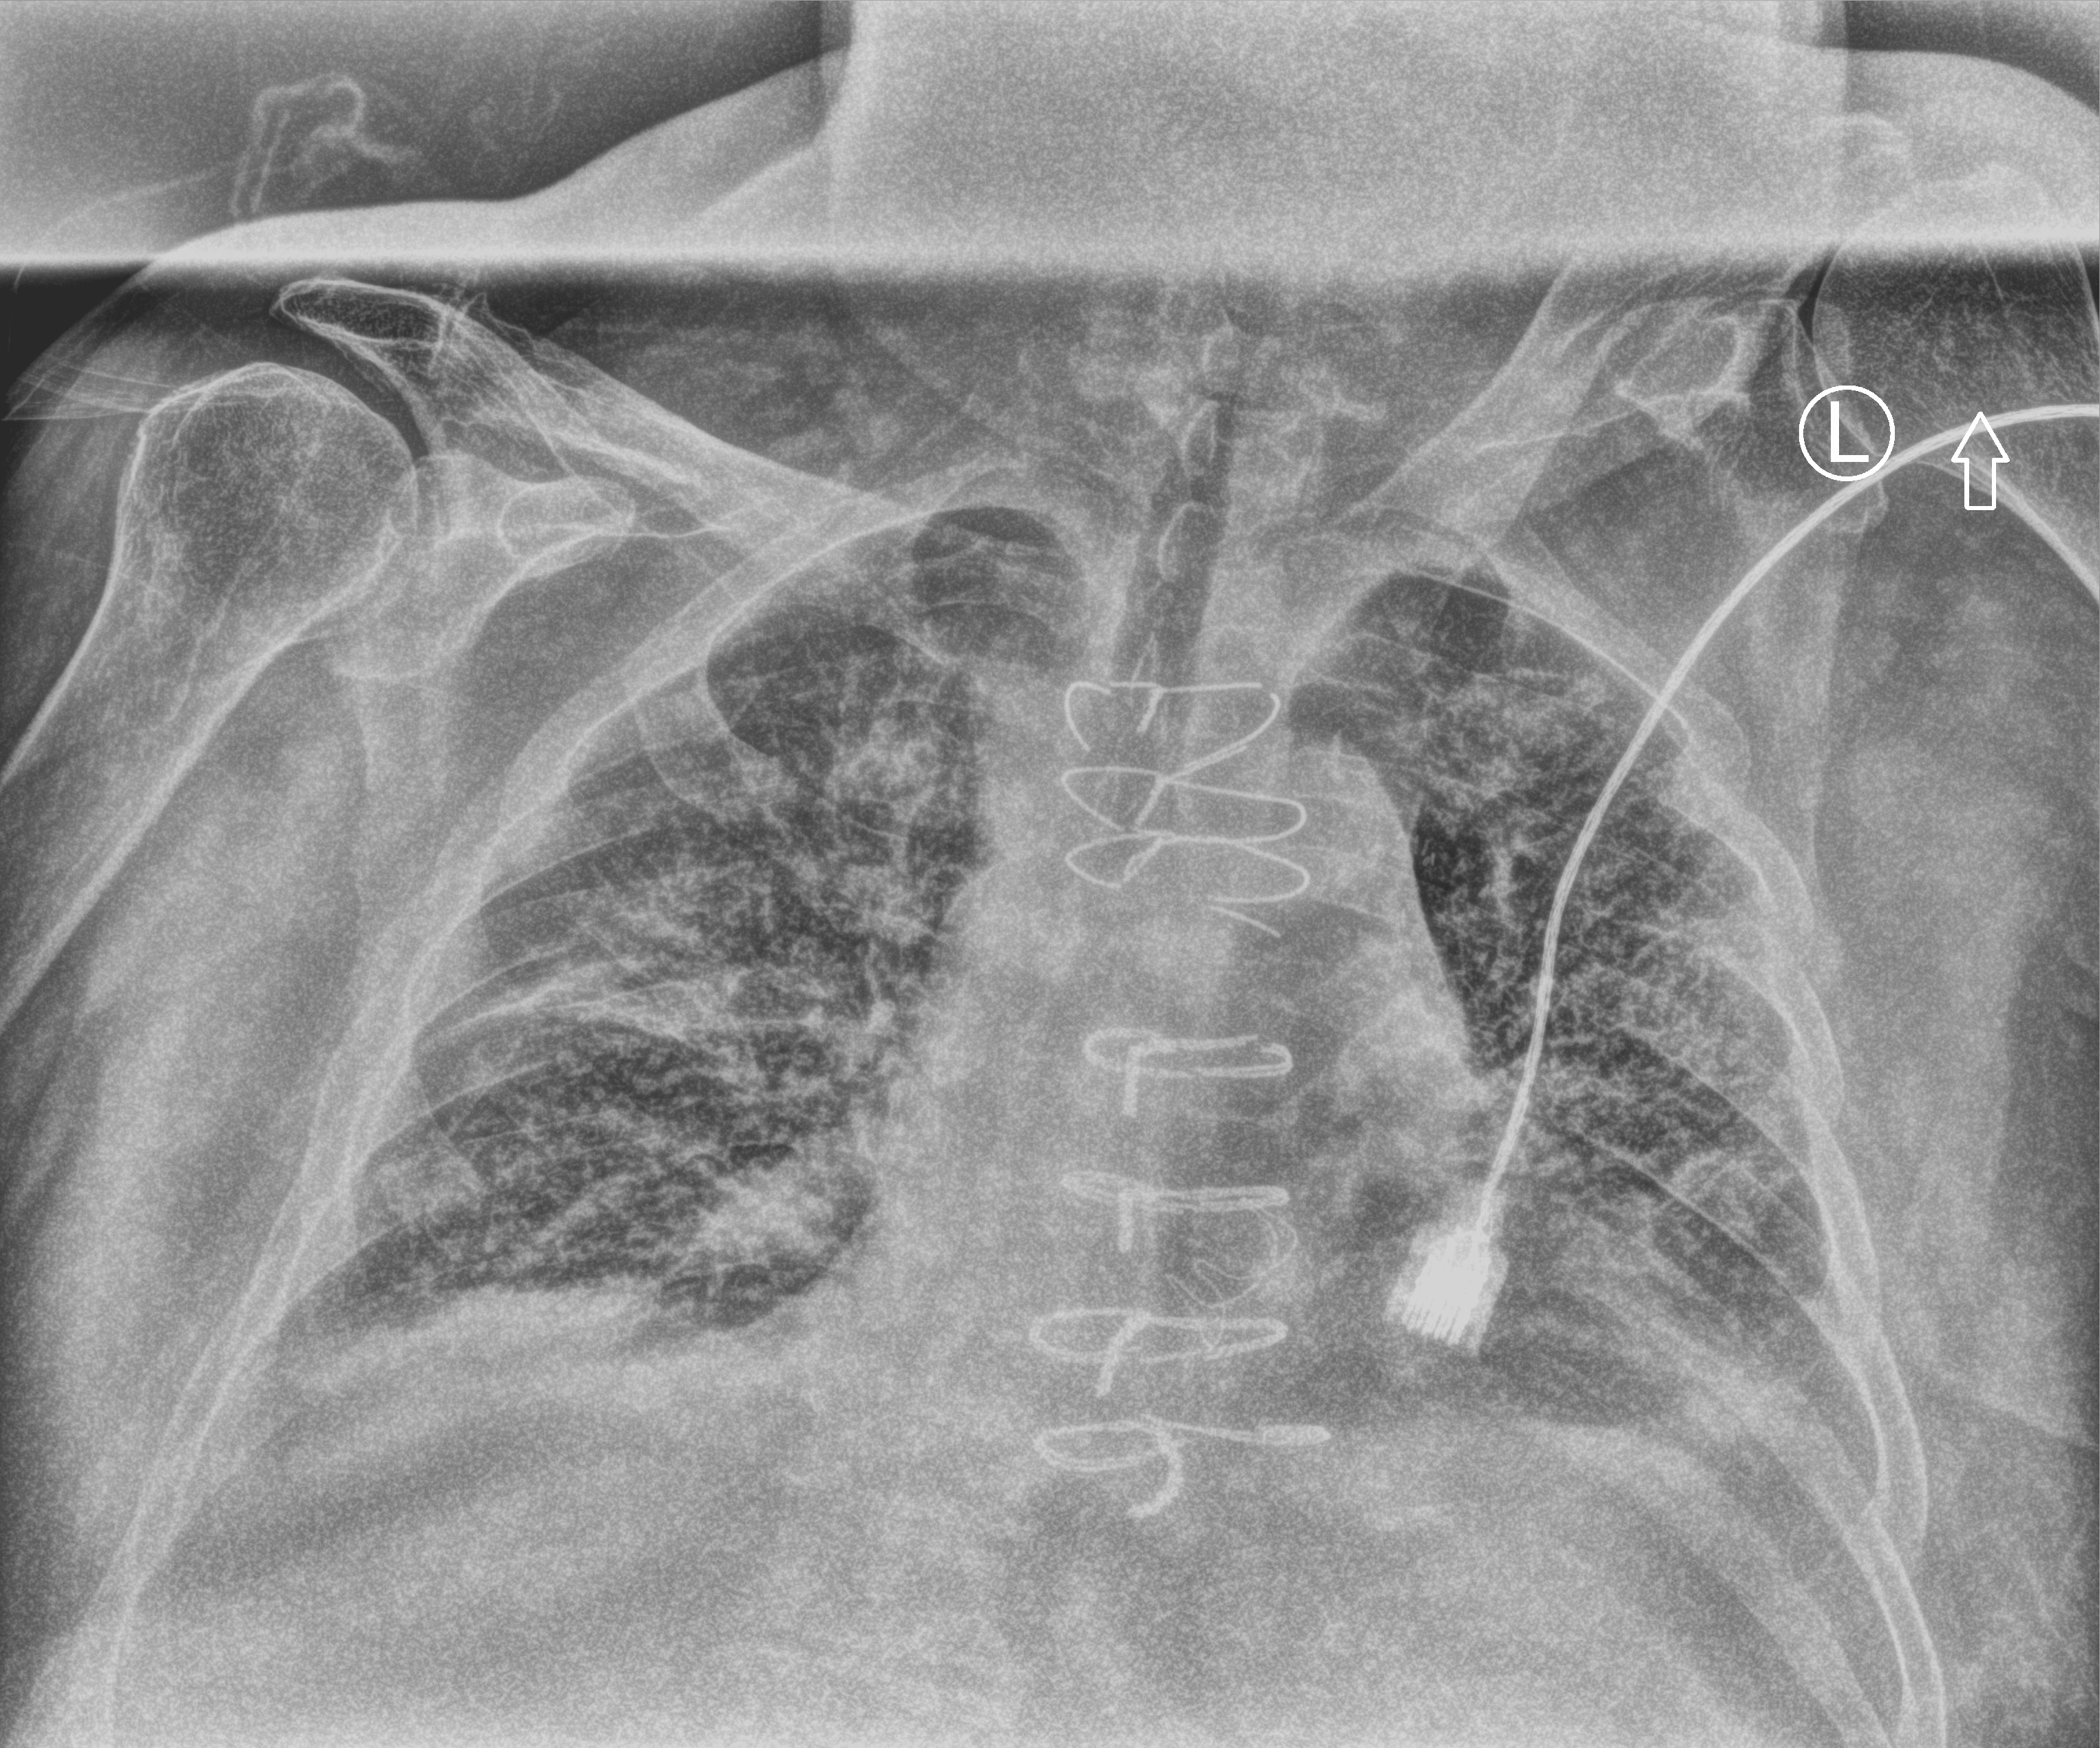
Portable chest radiograph; anteroposterior (AP) projection. Patient hospitalised with COVID-19; male, aged 75–90 years.
Hospital-stay facts (about this admission, not read from this image; timing relative to this image not recorded): smoking status (admission record): former; mechanically ventilated during this hospital stay: no; other chronic lung disease (admission record): yes.